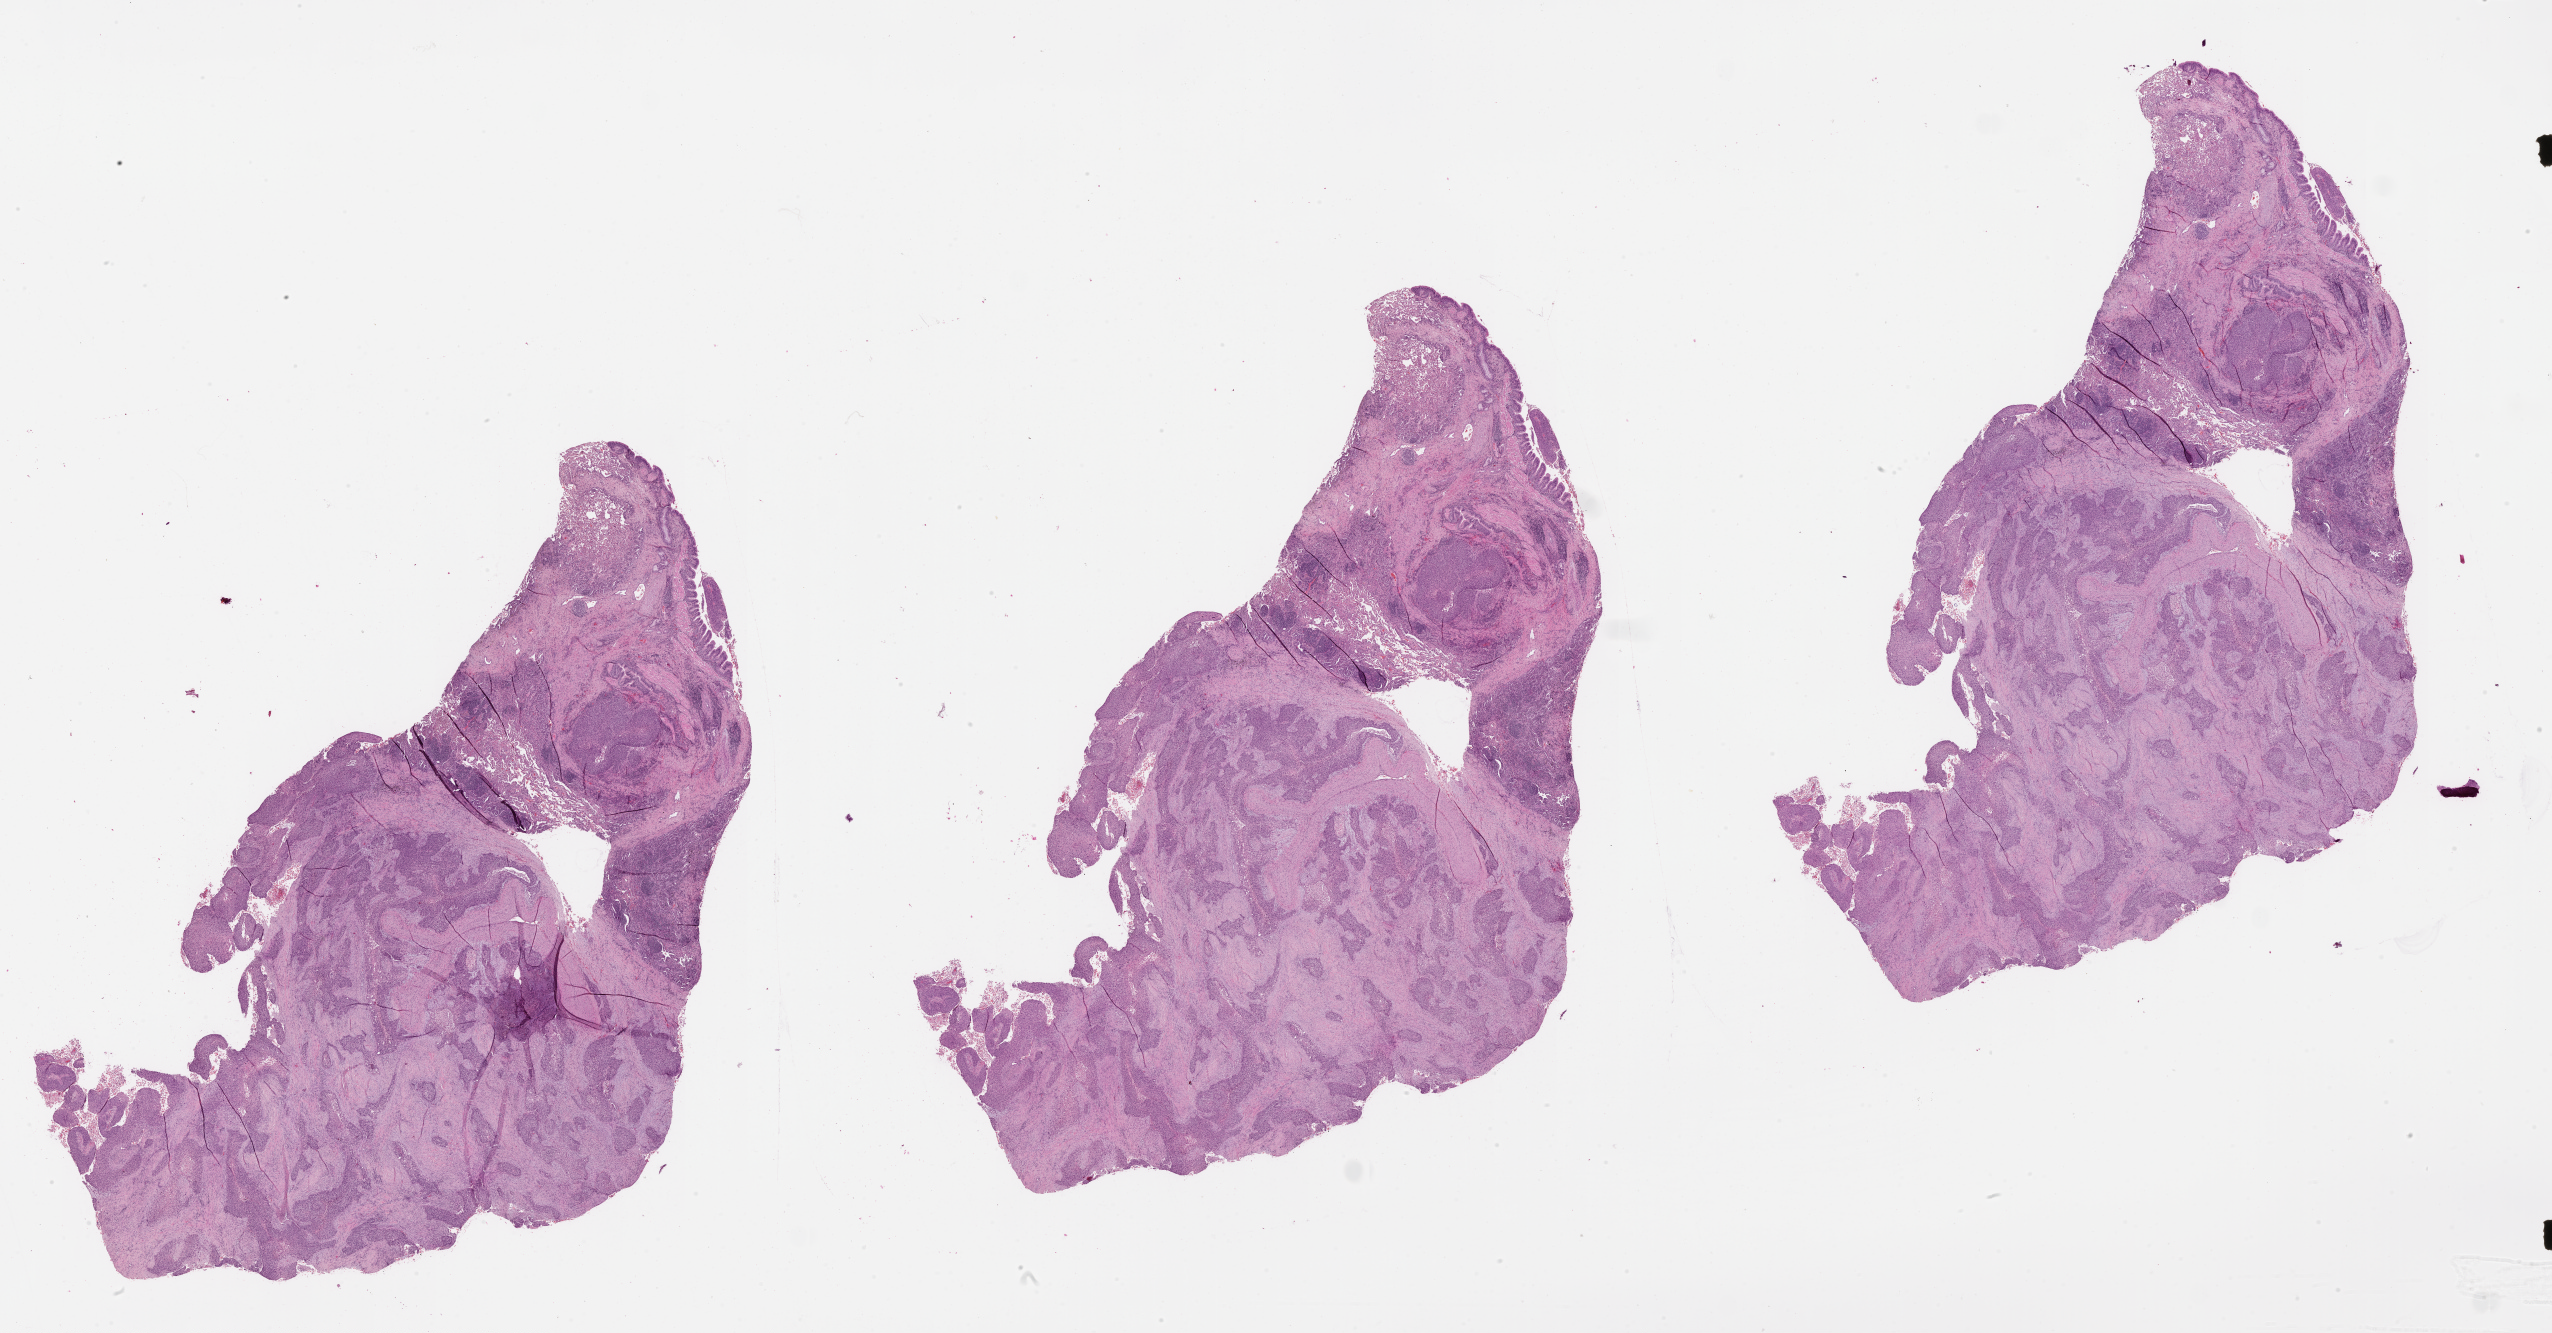
H&E whole-slide image, whole scanned area (about 41.1 x 21.5 mm) shown as a low-resolution overview. Lung, tumour tissue. Patient: male, age 43 years.
* patient diagnosis (cohort enrolment): squamous cell carcinoma (lung)